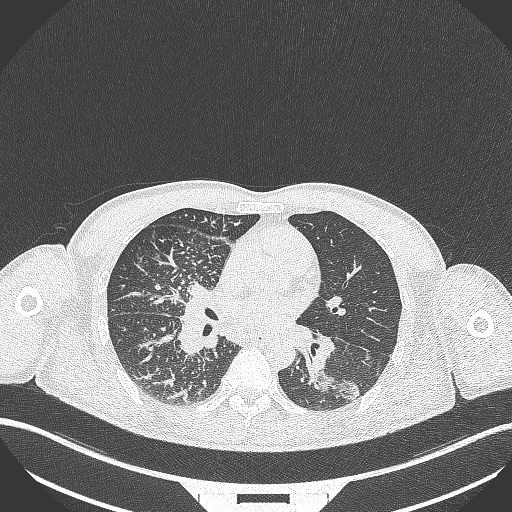
Chest CT, one axial slice; 120 kVp; lung window (W 1500 / L -600 HU); 1 mm slice thickness; 512 × 512 image matrix, field of view 400 × 400 mm. Patient: male, 49 years. From the clinical record (not read from this slice): clinical TNM (as recorded): T2b N1 M0.
Outlined on this slice (rectangle marked by the reading radiologist):
- lung tumour (recorded histology: adenocarcinoma): bounding box [x1, y1, x2, y2] px = [309, 365, 363, 405]